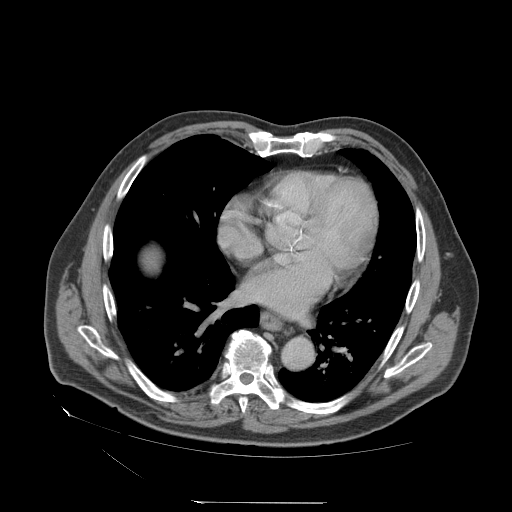
Contrast-enhanced abdominal CT (liver protocol), one axial slice; position 76 of 83 along the scan axis; 140 kVp; soft-tissue window (W 400 / L 40 HU); 2.5 mm slice thickness; 512 × 512 image matrix, field of view 460 × 460 mm. Case-level facts recorded for this patient, not image findings: diagnosis: hepatocellular carcinoma (patient treated with transarterial chemoembolisation; whether this scan precedes or follows treatment is not stated here); TNM stage (as recorded): Stage-I; Child-Pugh class: A; tumour differentiation: well differentiated; tumour nodularity: uninodular.
Annotated regions visible in this slice (semi-automatically segmented with operator editing):
- liver parenchyma outside the tumour (the mass and vessels are separate outlines, so this box may not span the whole liver): bounding box [x1, y1, x2, y2] px = [144, 250, 158, 269]